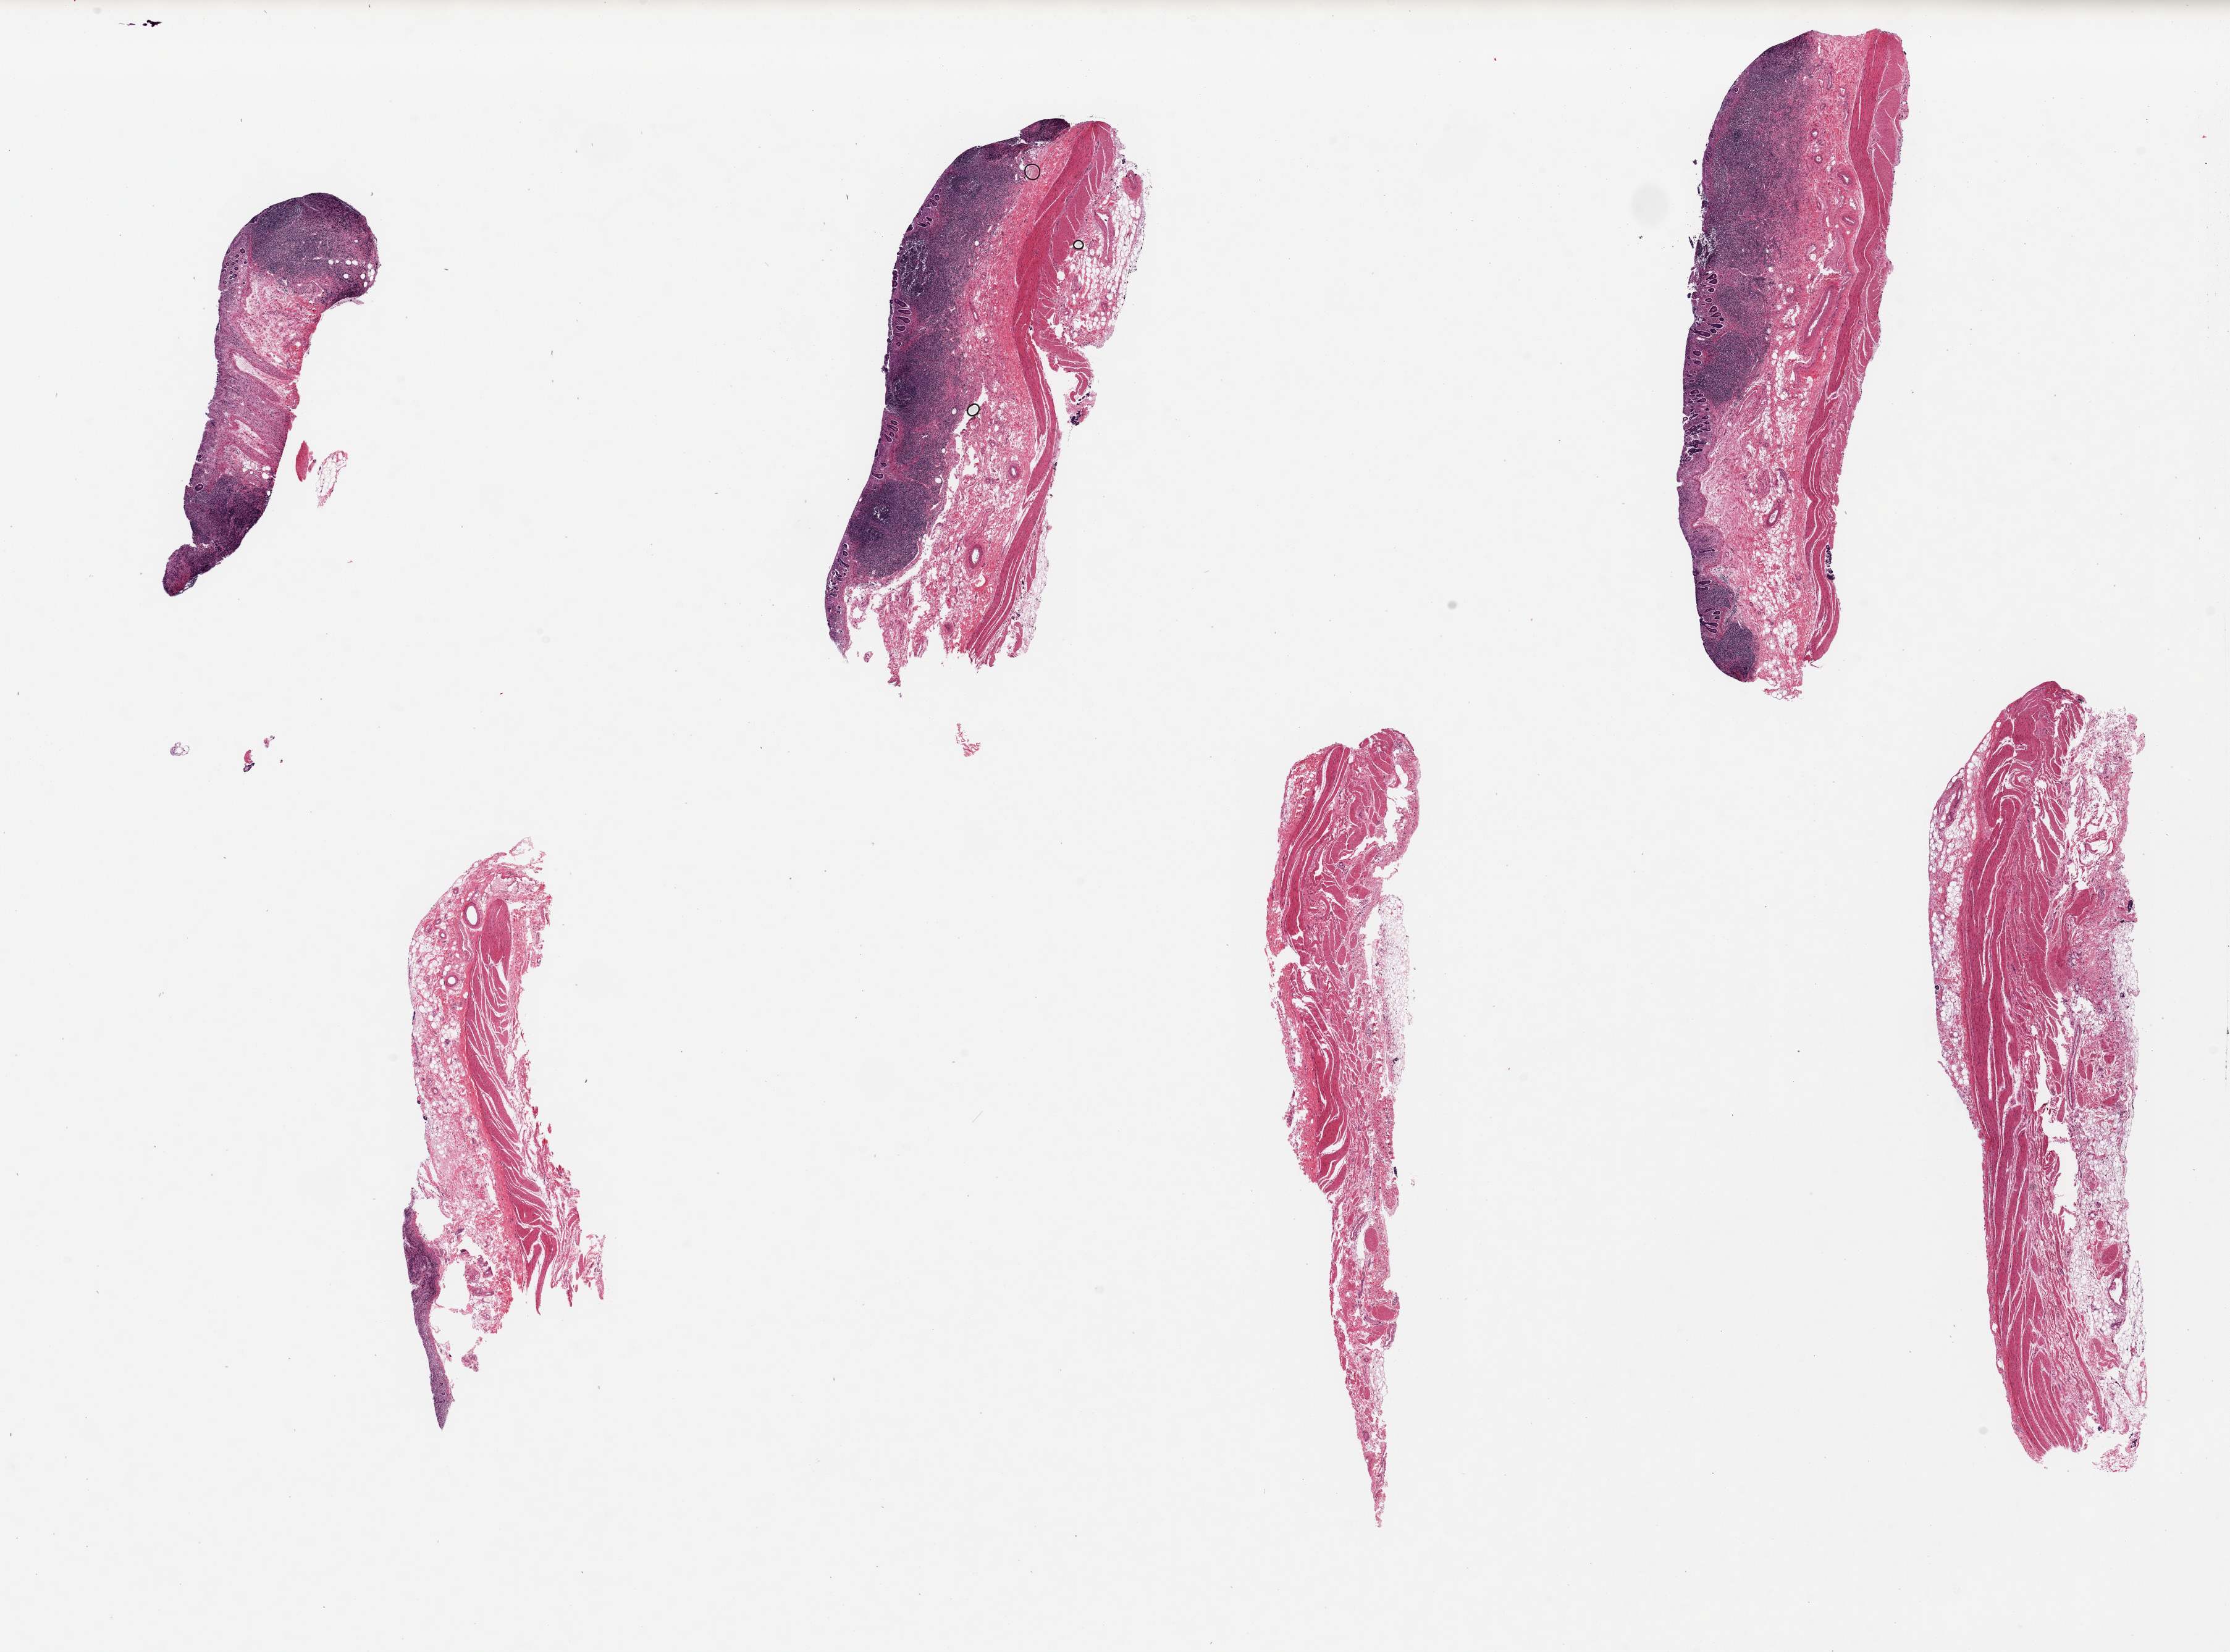
H&E whole-slide image, a low-resolution overview of the entire scanned area, about 28.5 x 21.2 mm (acquisition: 20x scan). PAXgene-fixed paraffin-embedded (PFPE) section. Target tissue: ileum. Tissue donor sample. Male donor.
• pathologist's review note for this sample: 6 pieces, up to 10x3mm; 3 pieces have good lymphoid tissue and some muscularis; 3 pieces have only muscularis; mucosa largely sloughed